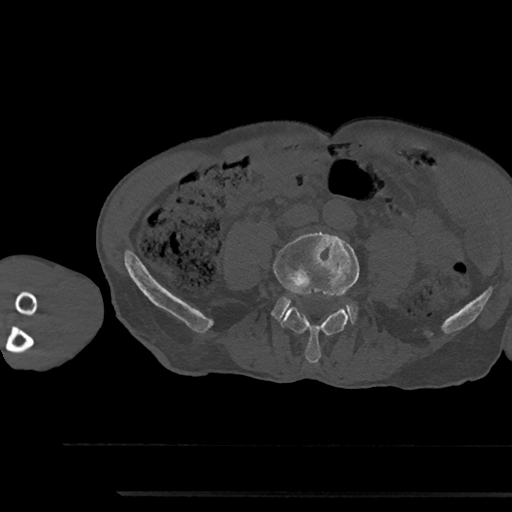
CT including the spine, one axial slice; position 392 of 797 along the scan axis; reconstruction kernel Br40s/3; 120 kVp; bone window (W 1800 / L 400 HU); 0.5 mm slice thickness; 512 × 512 image matrix, field of view 367 × 367 mm. Male patient, age 79 years. Case-level facts recorded for this patient, not image findings: primary cancer: prostate.
Structures marked on this image (semi-automatically segmented with operator editing):
- L4 vertebra: bounding box <274,232,359,364> (left, top, right, bottom; pixels)
- L5 vertebra: <273,297,357,323>